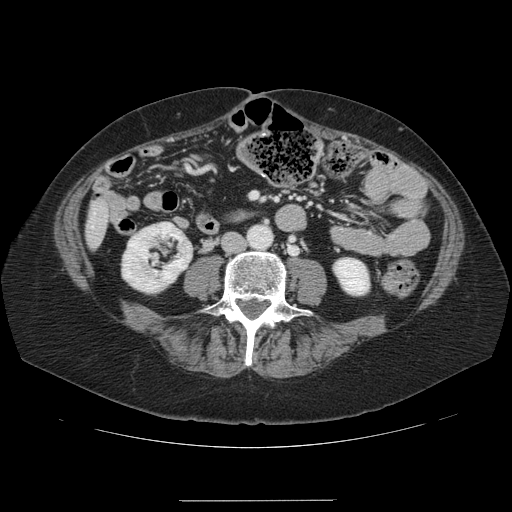
Contrast-enhanced abdominal CT, one axial slice; slice 13 of 141 in the series (ordered by position); 120 kVp; intravenous contrast given; soft-tissue window (W 400 / L 40 HU); 2.5 mm slice thickness; 512 × 512 image matrix, field of view 393 × 393 mm. Female patient, age 74 years. Case-level facts recorded for this patient, not image findings: diagnosis: colorectal cancer liver metastases, imaged before liver resection.
Annotated regions visible in this slice (expert manual segmentation):
- liver: box from (x=87, y=201) to (x=109, y=247) px
- planned liver remnant (the part of the liver to remain after resection): (x=90, y=234)–(x=106, y=247)